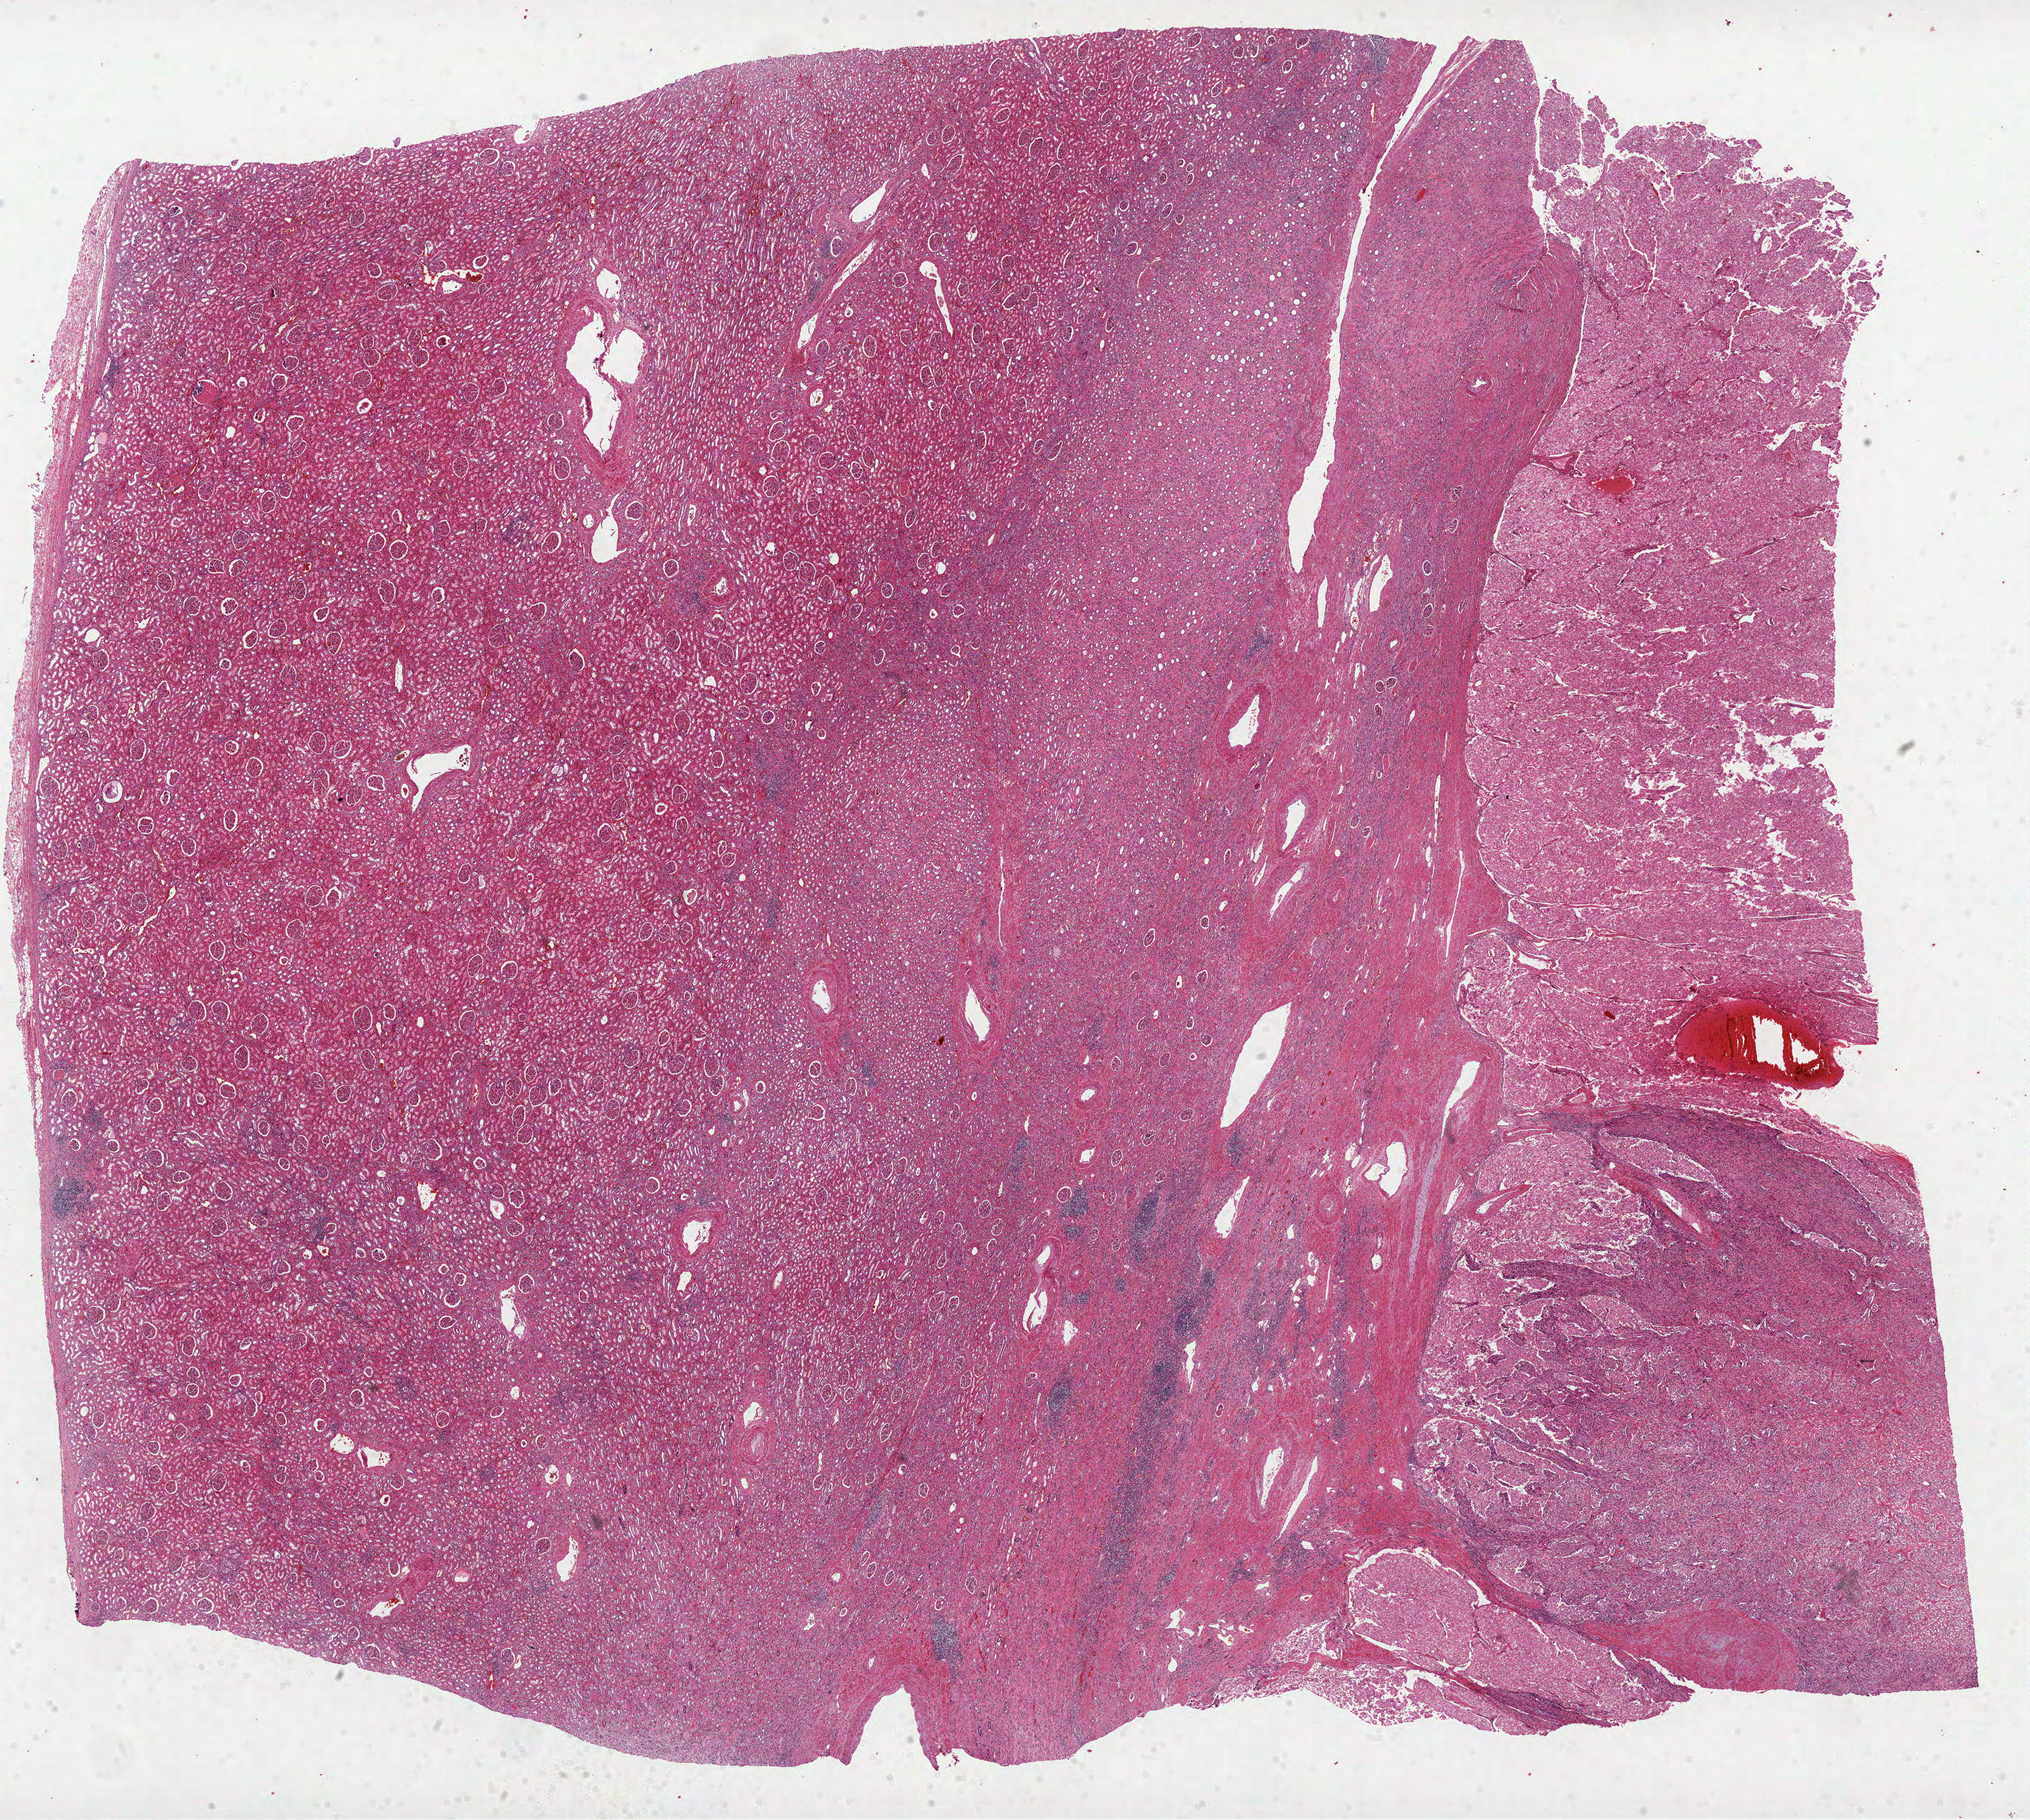
Whole-slide histology image, Hematoxylin and eosin (H&E) stained, shown as a low-resolution overview of the whole scanned area (about 23.2 x 20.8 mm); formalin-fixed paraffin-embedded (FFPE) diagnostic section; kidney, primary tumour sample. Male patient; age at initial diagnosis 74 years. Histologic grade: G4 (undifferentiated).
TNM: T4 N0 M1. Histologic diagnosis: Clear cell adenocarcinoma, NOS. Lymph nodes positive (case pathology): 0 of 6 examined. AJCC pathologic stage: IV.